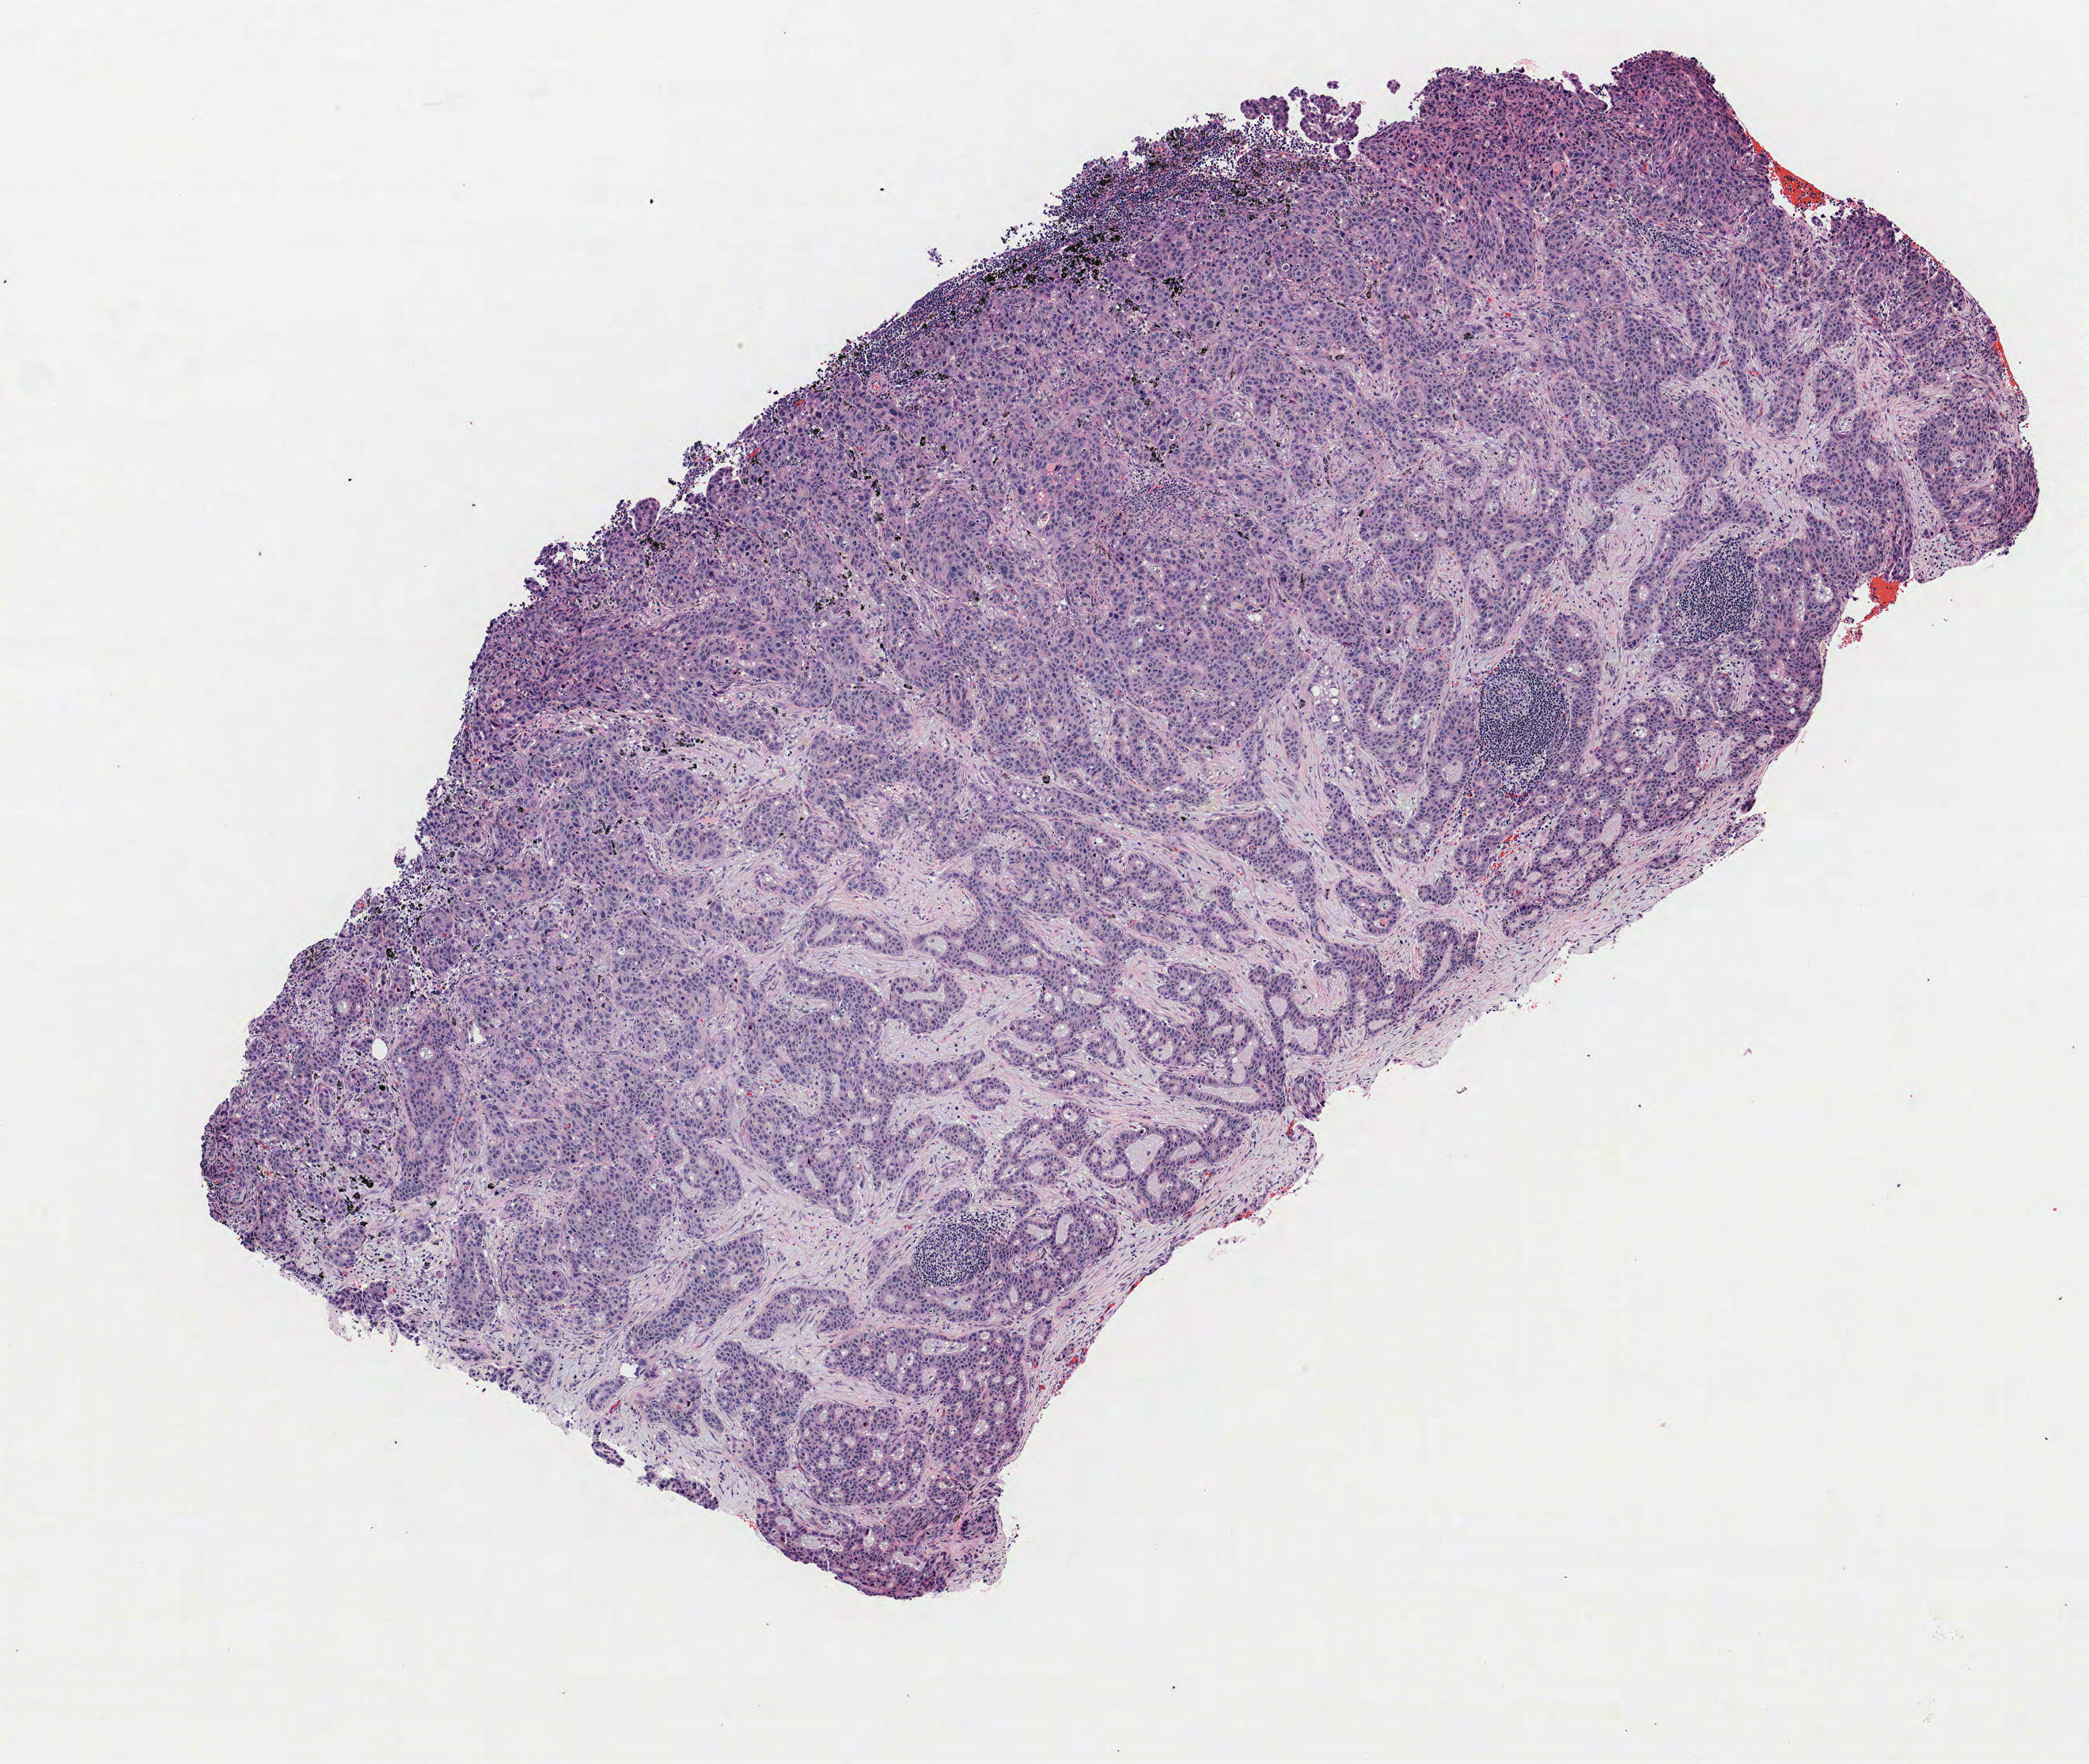
Hematoxylin and eosin (H&E) stained whole-slide image — low-resolution overview of the scanned area, about 5.3 x 4.5 mm (acquisition: 40x scan); formalin-fixed paraffin-embedded (FFPE) section; lung tissue. Male patient, aged 60 at enrolment. Grade: poorly differentiated (G3).
Tumour size (pathology): 20 mm. Participant's lung-cancer diagnosis: Adenocarcinoma, NOS. Stage (AJCC 6th edition): IIIA. Primary tumour location (clinical record): left upper lobe. ICD-O-3 topography: upper lobe of lung (C34.1).